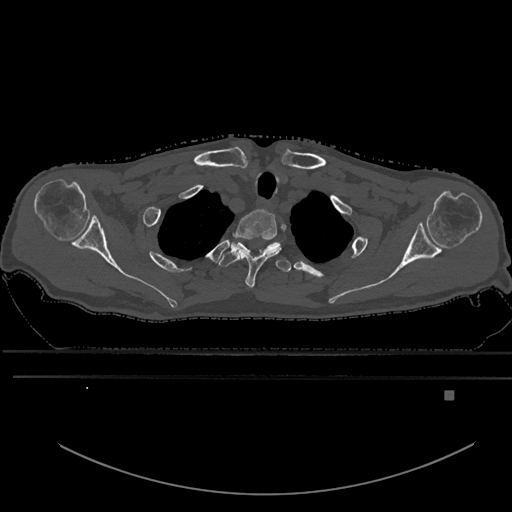
CT including the spine, one axial slice. Position 519 of 969 along the scan axis. Bone window (W 1800 / L 400 HU). 512 × 512 image matrix, field of view 456 × 456 mm. Male patient, age 82 years. Case-level facts recorded for this patient, not image findings: primary cancer: prostate; vertebrae with lytic lesions (as recorded): T11, T9, T8, T2.
Structures marked on this image (semi-automatically segmented with operator editing):
- T1 vertebra: bounding box <235,209,281,290> (left, top, right, bottom; pixels)
- T2 vertebra: <219,238,280,267>